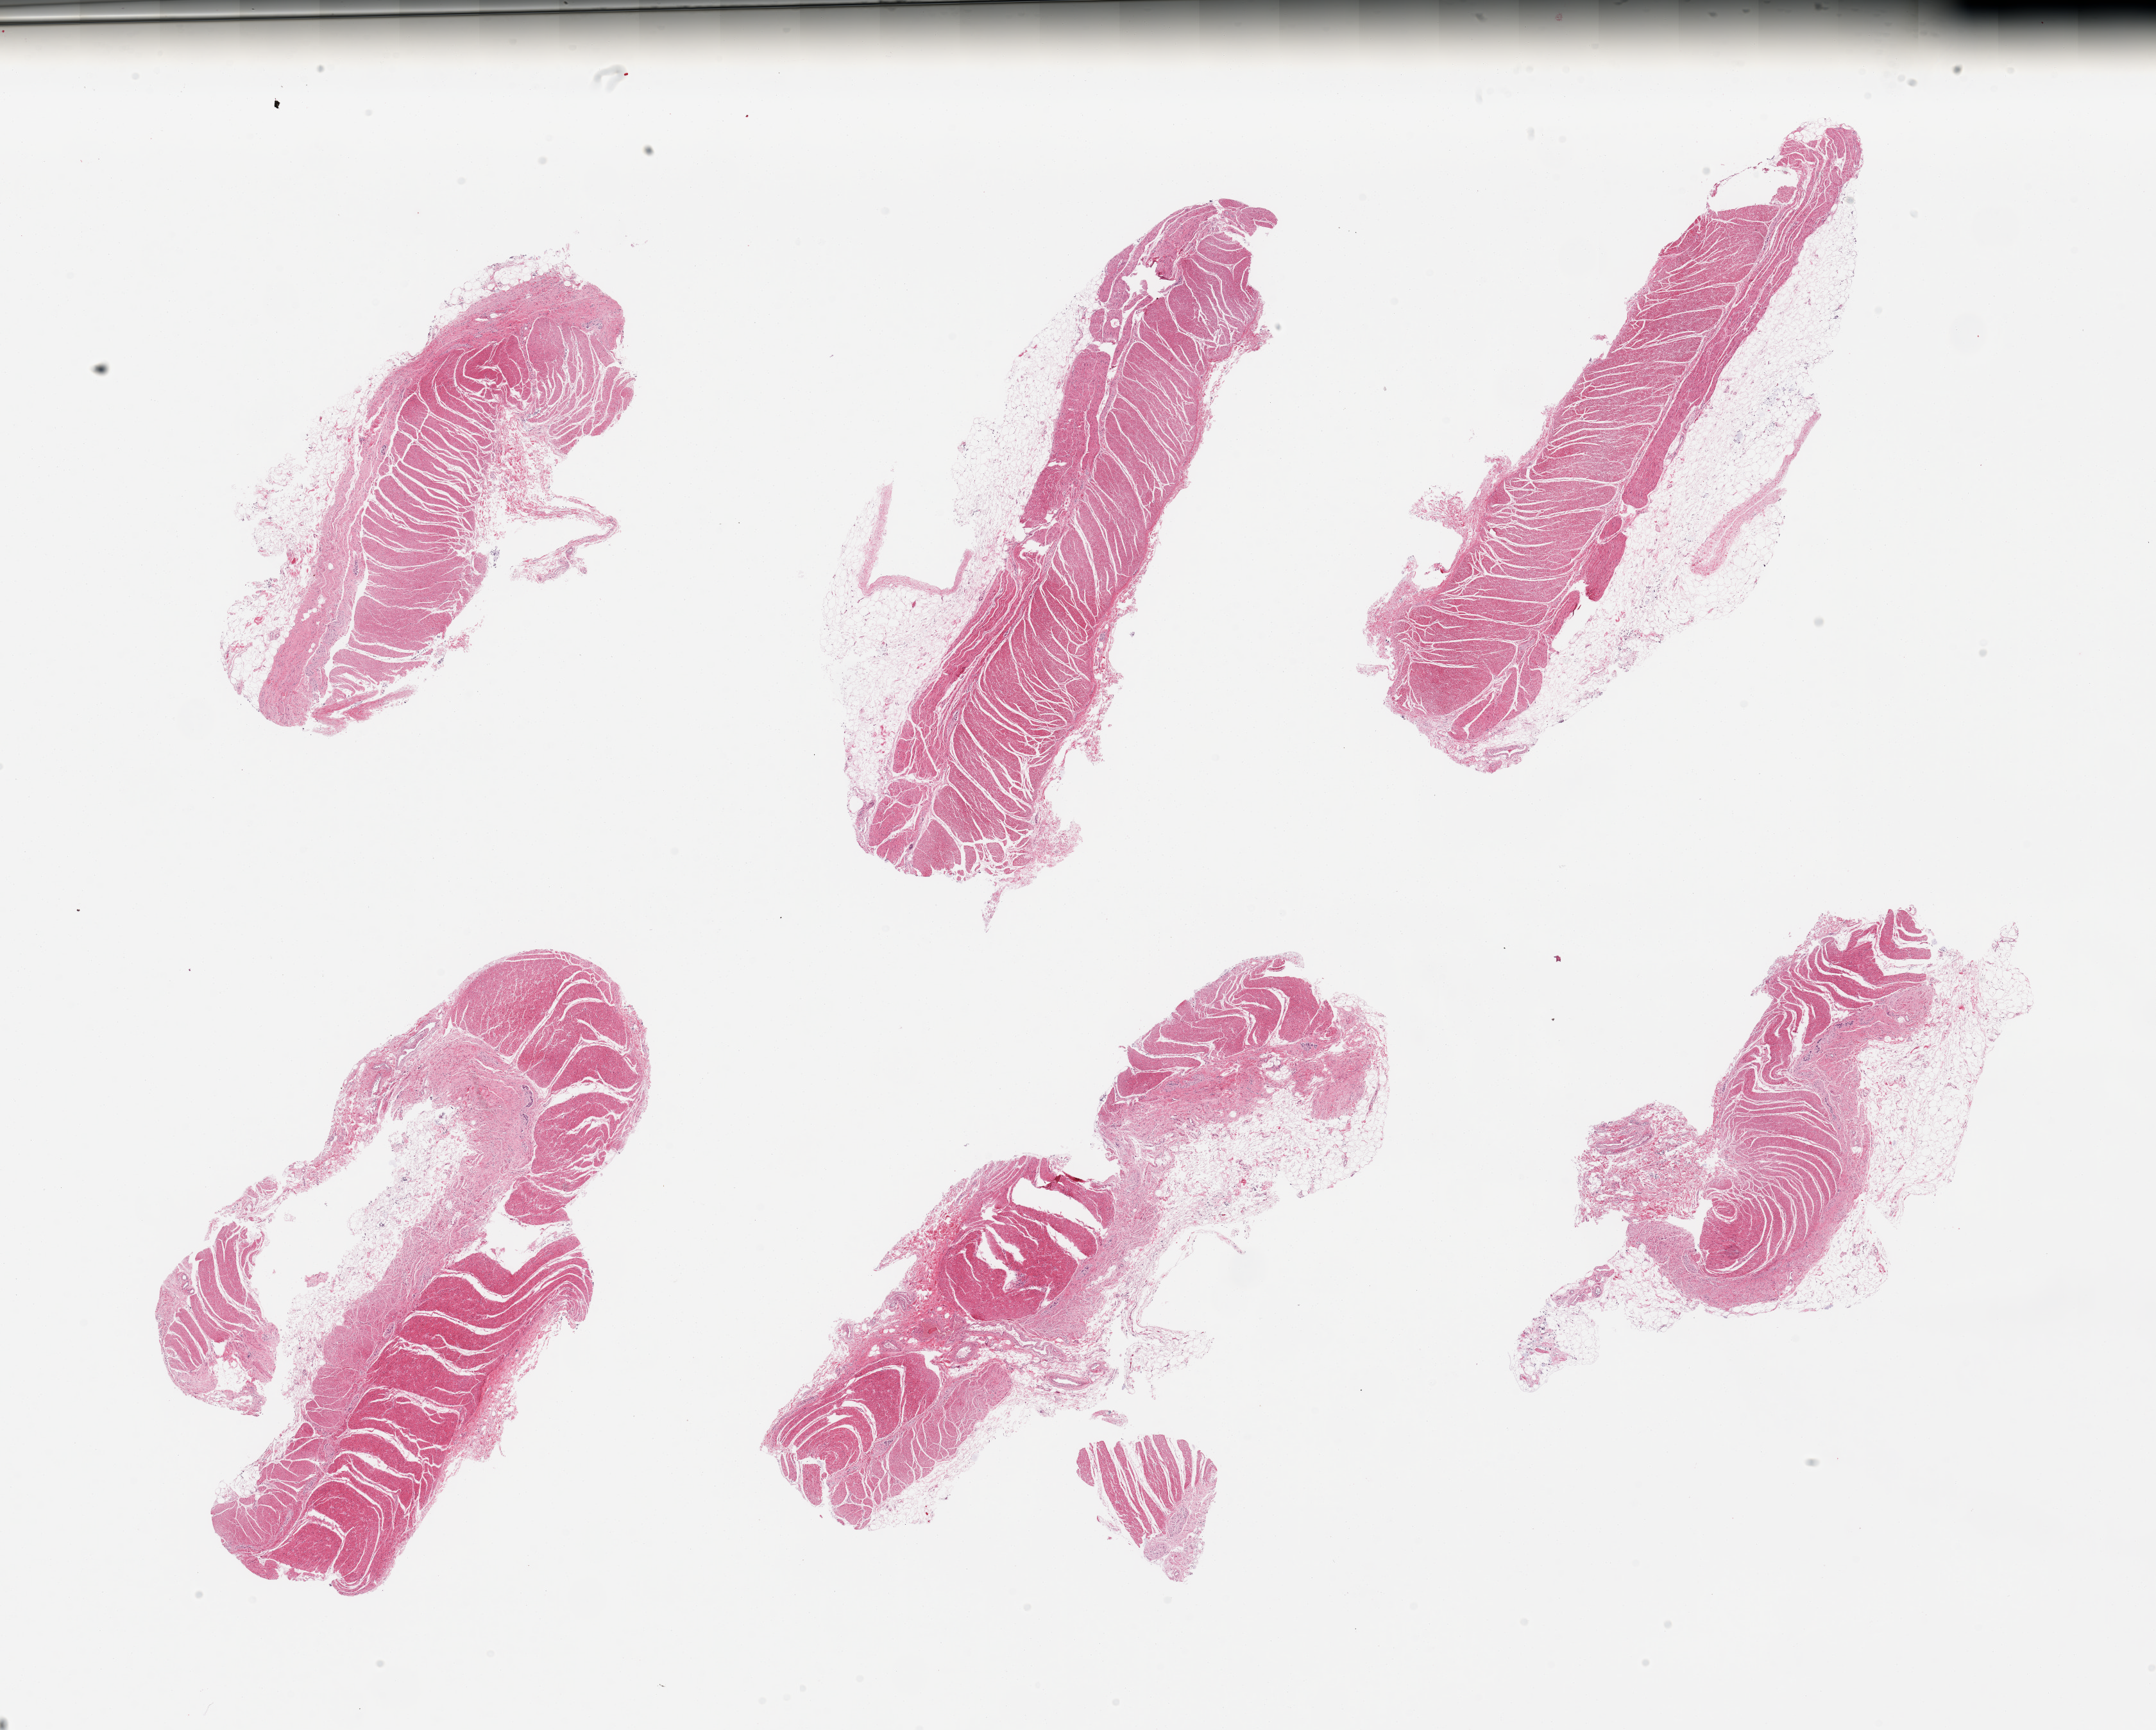
Hematoxylin and eosin (H&E) whole-slide image, brightfield — shown as a low-resolution overview of the whole scanned area (about 26.6 x 21.3 mm), PAXgene-fixed, paraffin-embedded tissue, target tissue: ileum, donor tissue sample.
• pathologist's review note for this sample: 6 pieces; moderately autolyzed muscularis